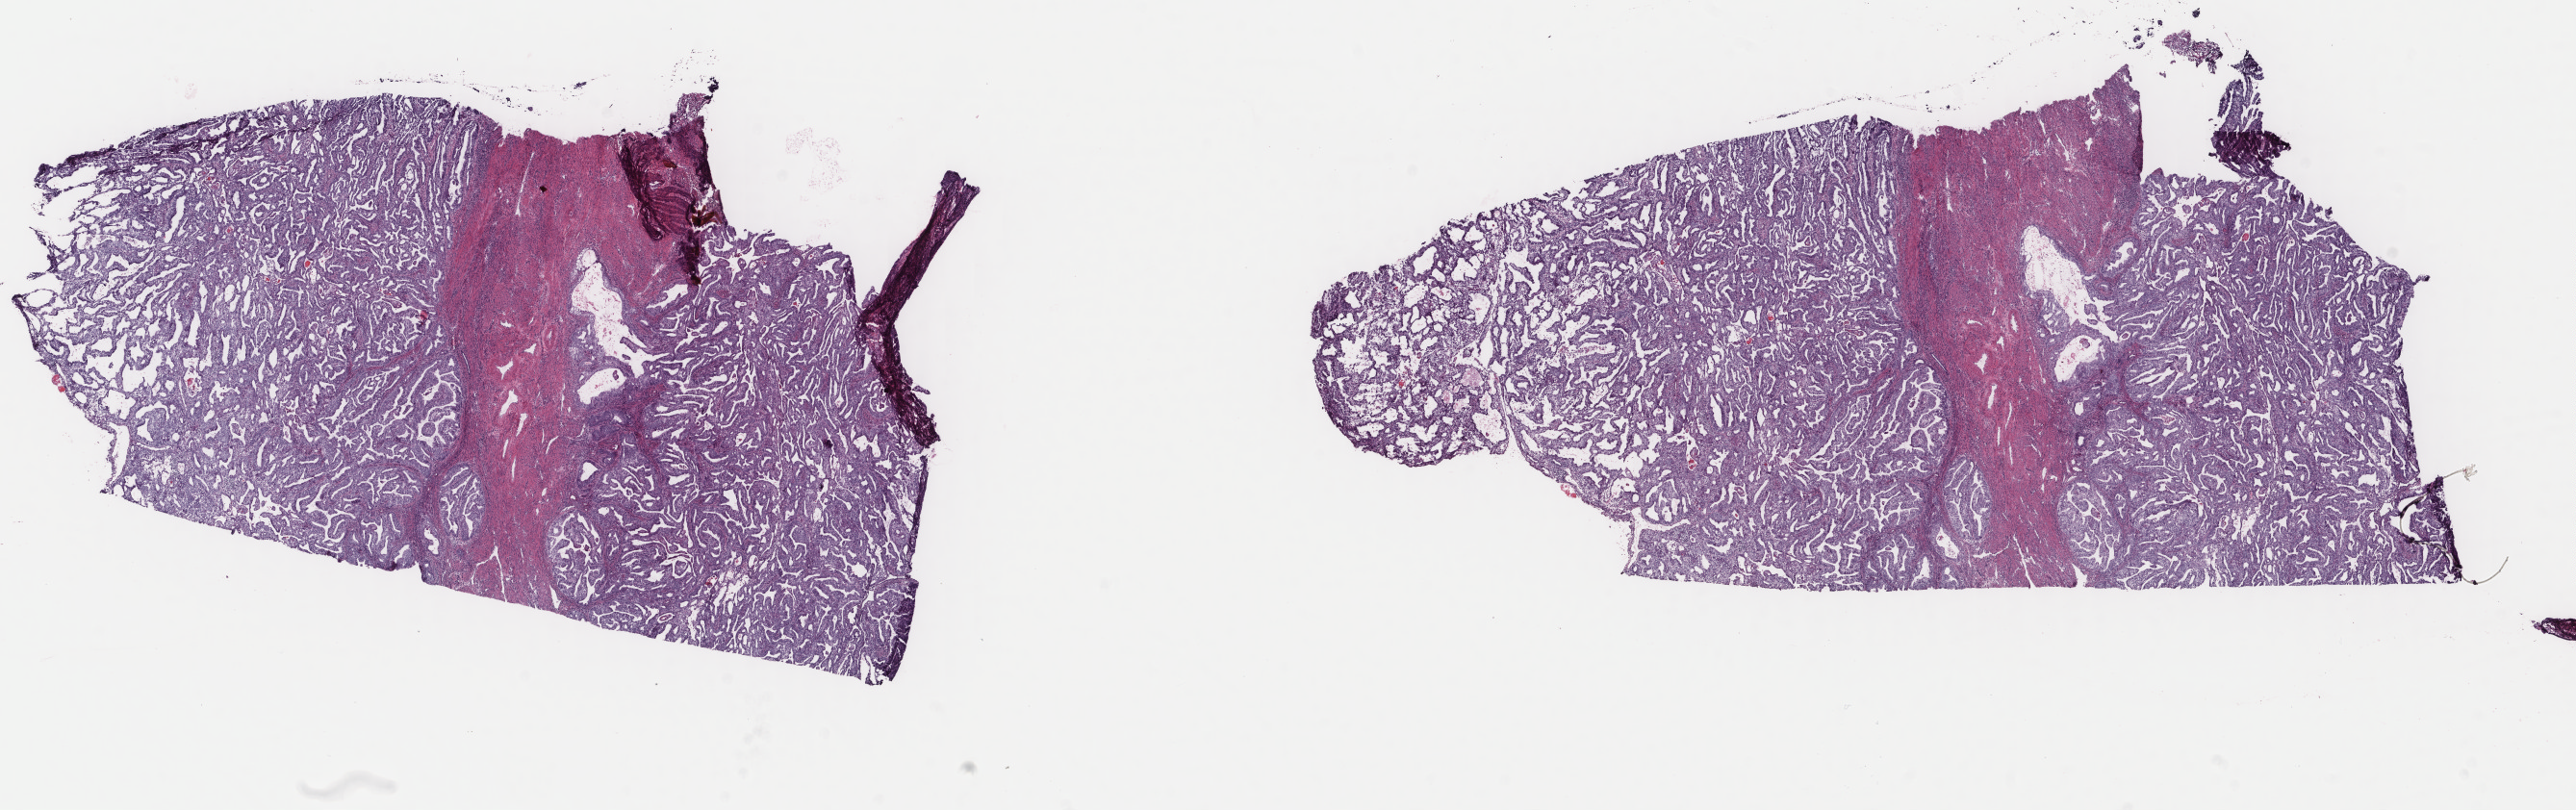
Digitized H&E tissue section (whole slide), a low-resolution overview of the entire scanned area, about 21.2 x 6.7 mm (slide scanned at 40x); frozen section; uterus, primary tumour sample. Female patient; age at initial diagnosis 60 years. Histologic grade: G1 (well differentiated). Pathologist review of this section (percent, as recorded): tumour cells 60%, tumour nuclei 60%, normal cells 2%, stromal cells 38%, necrosis 0%. Infiltration values recorded for this section: lymphocyte infiltration 8%, monocyte infiltration 0%, neutrophil infiltration 1%.
* FIGO stage: IA
* pathologic diagnosis: Endometrioid adenocarcinoma, NOS